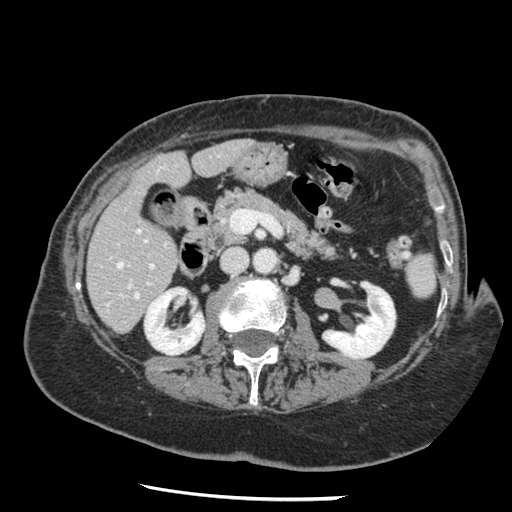
Contrast-enhanced abdominal CT, one axial slice; position 58 of 148 along the scan axis; reconstruction kernel STANDARD; 120 kVp; intravenous contrast given; soft-tissue window (W 400 / L 40 HU); 2.5 mm slice thickness; 512 × 512 image matrix, field of view 330 × 330 mm. Female patient, age 85 years. From the clinical record (not read from this slice): diagnosis: colorectal cancer liver metastases, imaged before liver resection; multiple liver metastases: no; largest metastasis: 0.9 cm.
Annotated regions visible in this slice (manually delineated by an expert):
- hepatic veins: bounding box <117,230,141,298> (left, top, right, bottom; pixels)
- liver: <88,140,249,333>
- planned liver remnant (the part of the liver to remain after resection): <90,140,249,333>
- portal vein (with intrahepatic branches): <151,265,153,267>